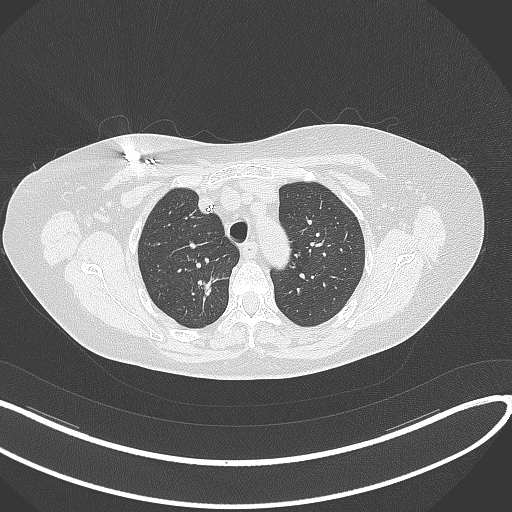
Chest CT, one axial slice. Slice 261 of 316 in the series (ordered by position). Lung window (W 1500 / L -600 HU). 1 mm slice thickness. 512 × 512 image matrix. Patient: female, 72 years. Case-level facts recorded for this patient, not image findings: clinical TNM (as recorded): T1c N0 M0.
Outlined on this slice (rectangle marked by the reading radiologist):
- lung tumour (recorded histology: adenocarcinoma): bounding box <187,270,228,306> (left, top, right, bottom; pixels)